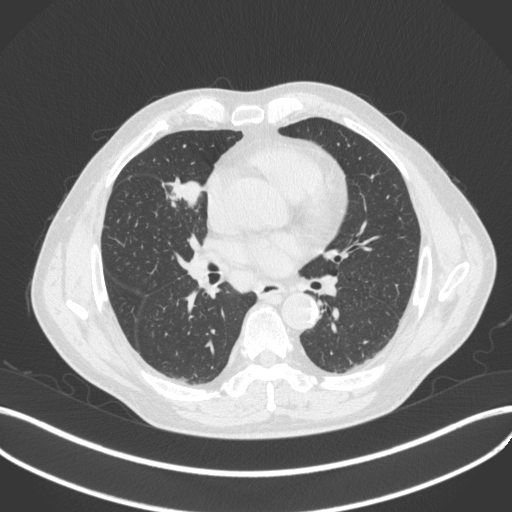
Chest CT, one axial slice. Position 202 of 429 along the scan axis. Reconstruction kernel B31f. Lung window (W 1500 / L -600 HU). 1 mm slice thickness. 512 × 512 image matrix, field of view 400 × 400 mm. Patient: male, 61 years. From the clinical record (not read from this slice): clinical TNM (as recorded): T2b N1 M0.
Structures marked on this image (rectangle marked by the reading radiologist):
- lung tumour (recorded histology: squamous cell carcinoma): bounding box <167,176,204,209> (left, top, right, bottom; pixels)